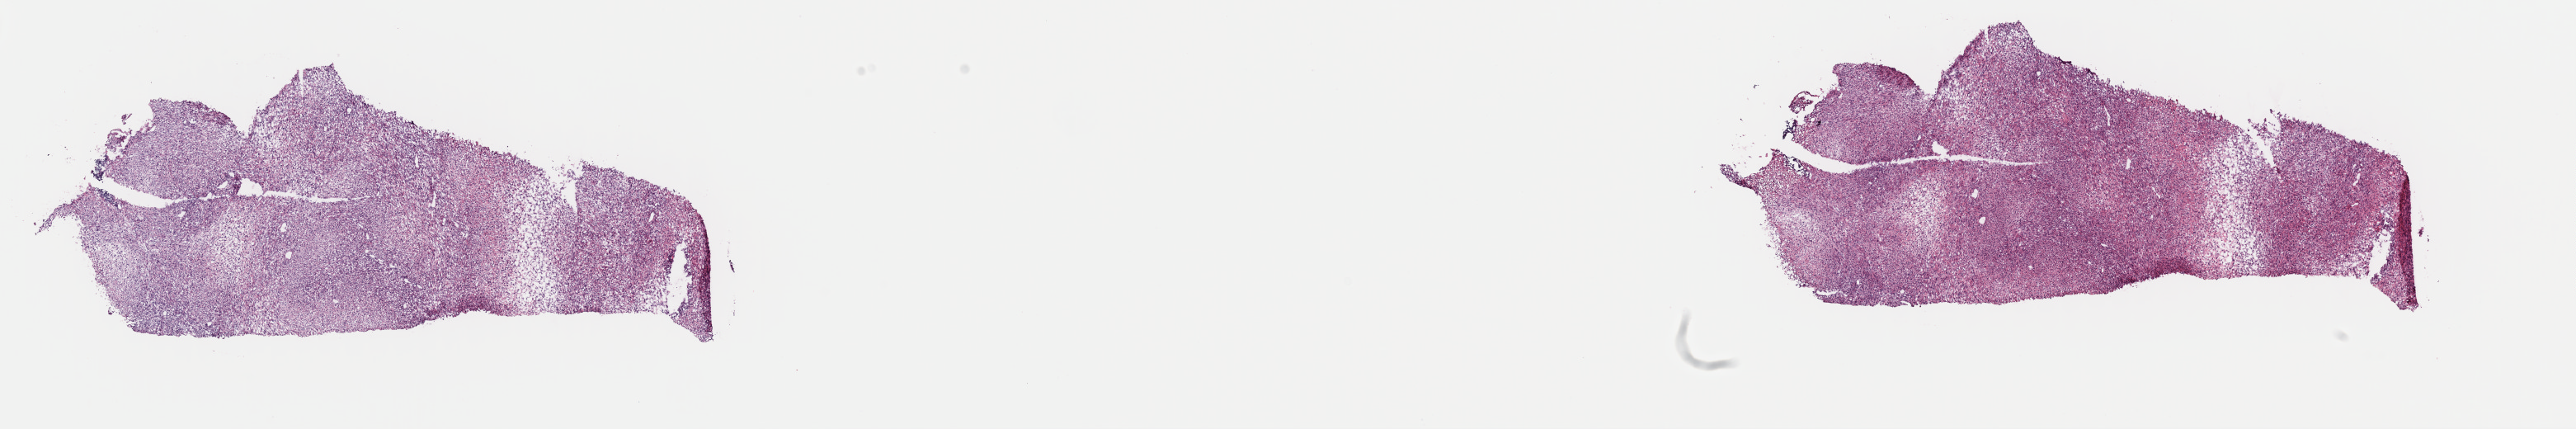
Digitized H&E-stained tissue section (whole slide) — whole scanned area (about 24.7 x 4.1 mm, from a 40x scan) shown as a low-resolution overview. Frozen section from the top of the tissue portion. Primary tumour sample from the retroperitoneum and peritoneum. Female patient; age at initial diagnosis 78 years. Slide review estimates, as recorded: tumour cells 50%, tumour nuclei 100%, normal cells 0%, stromal cells 50%, necrosis 0%. Infiltration values recorded for this section: lymphocyte infiltration 0%, monocyte infiltration 0%, neutrophil infiltration 0%.
Histologic diagnosis: Dedifferentiated liposarcoma (retroperitoneum).